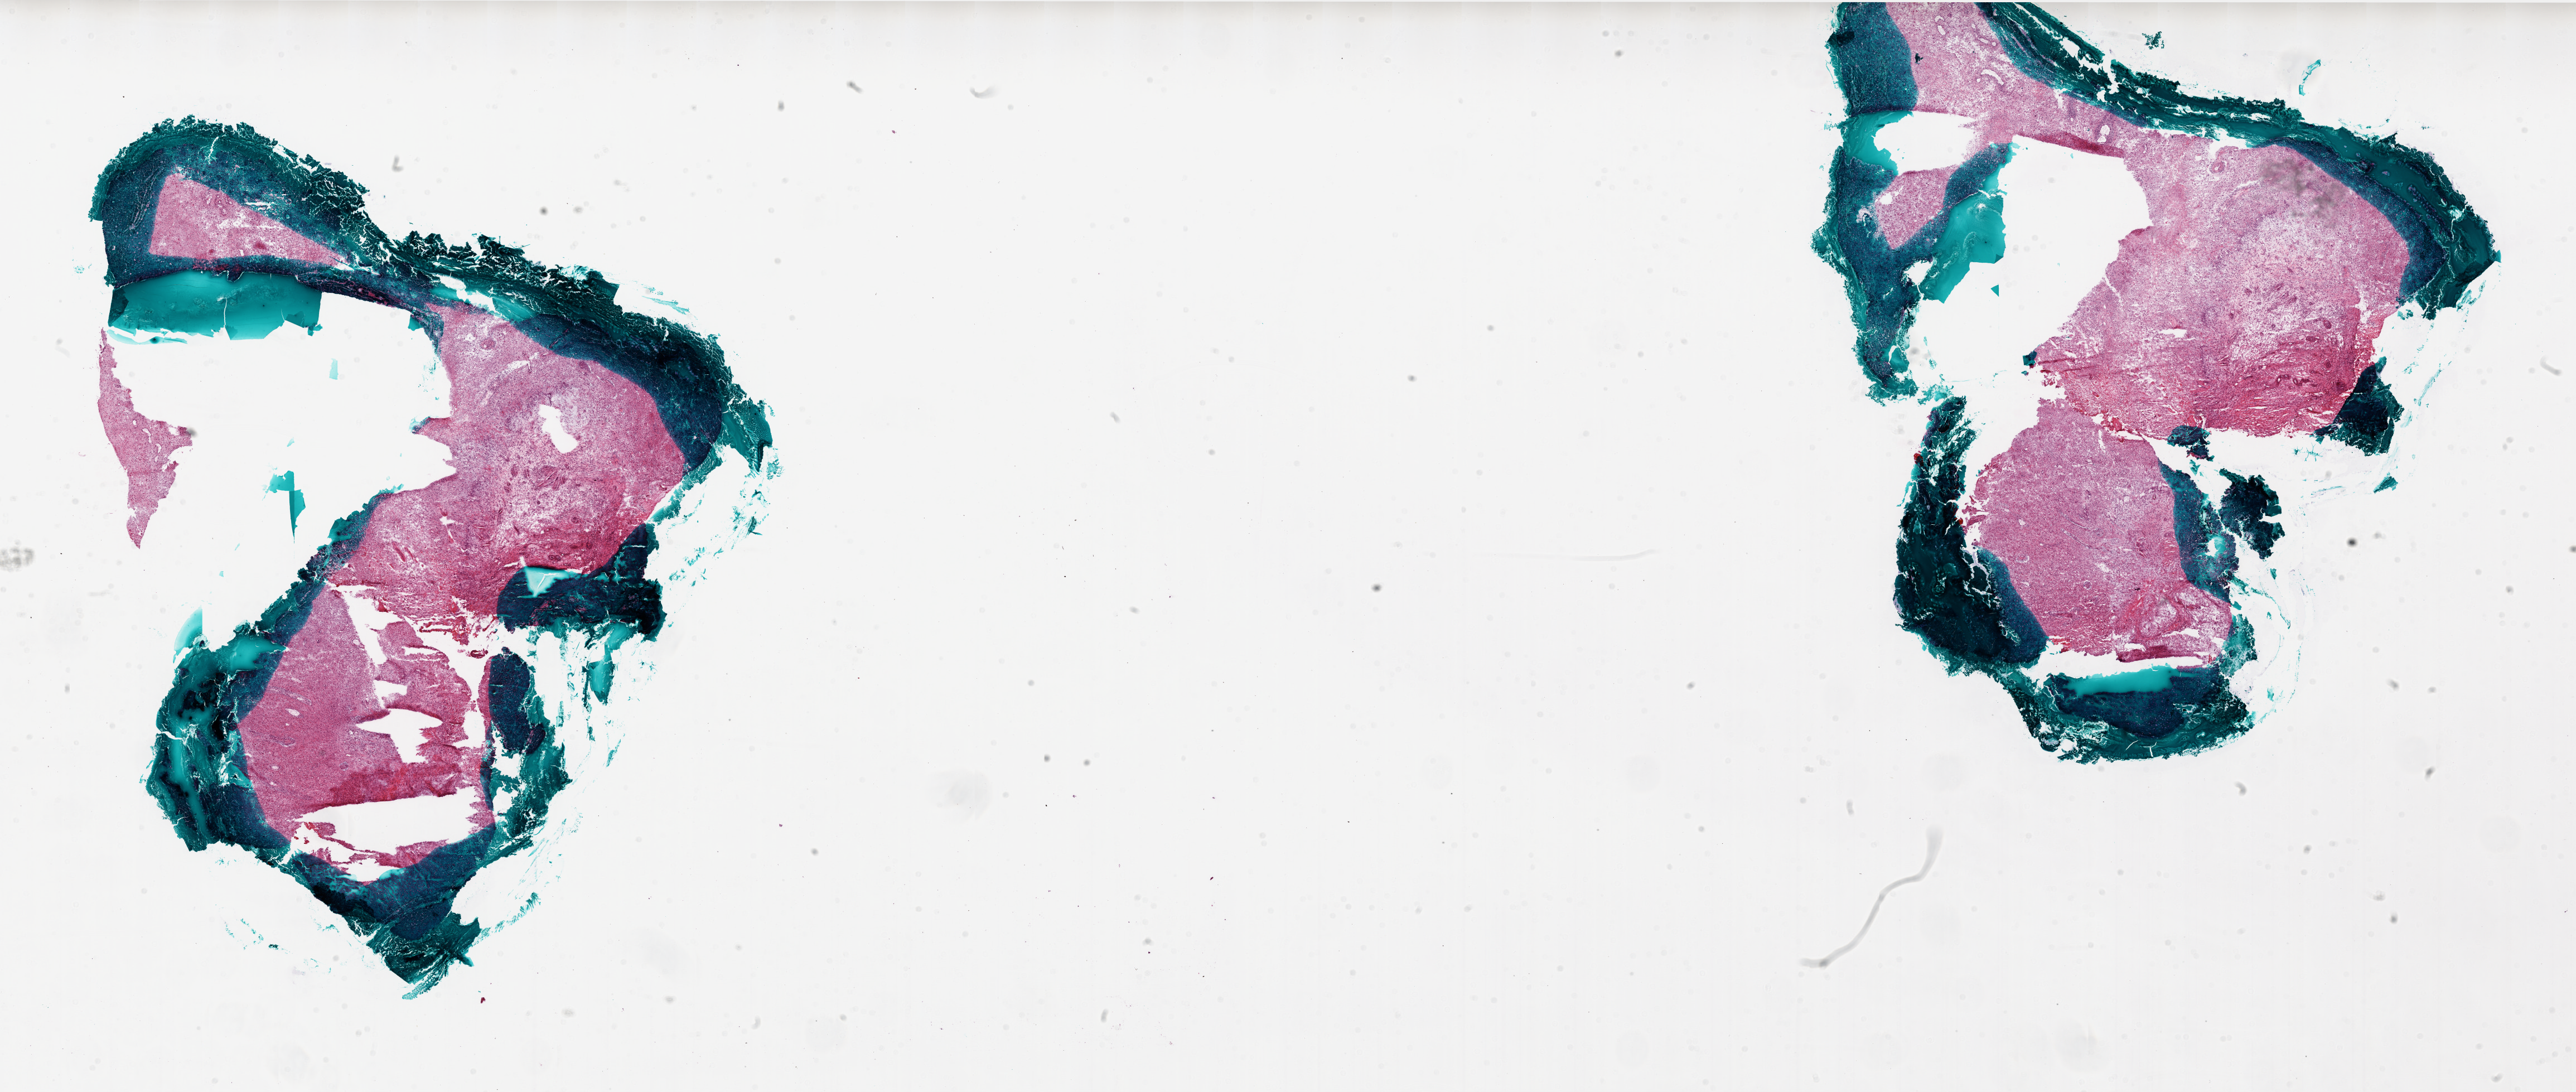
Digitized H&E-stained tissue section (whole slide), a low-resolution overview of the entire scanned area, about 37.0 x 15.7 mm (from a 20x scan); frozen section from the bottom of the tissue portion; brain, primary tumour sample. Patient: male, age at initial diagnosis 56 years. Slide review estimates, as recorded: tumour cells 80%, tumour nuclei 95%, normal cells 0%, stromal cells 10%, necrosis 10%.
Diagnosis: Glioblastoma.